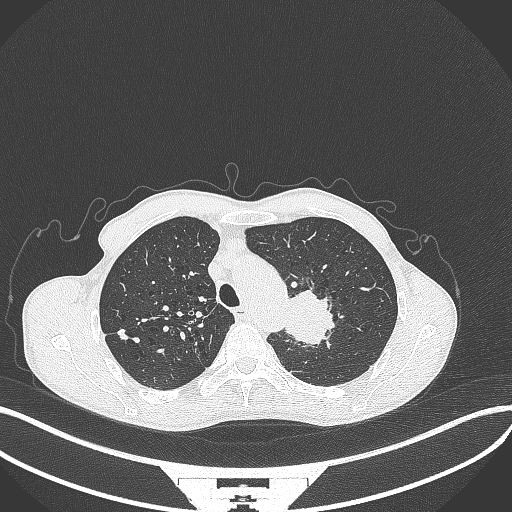
Chest CT, one axial slice; slice 324 of 386 in the series (ordered by position); 120 kVp; lung window (W 1500 / L -600 HU); 1 mm slice thickness; 512 × 512 image matrix, field of view 400 × 400 mm. Patient: male, 65 years. From the clinical record (not read from this slice): clinical TNM (as recorded): T2b N0 M0.
Structures marked on this image (rectangle marked by the reading radiologist):
- lung tumour (recorded histology: adenocarcinoma): bounding box (x1, y1, x2, y2) in pixels: (281, 286, 339, 348)